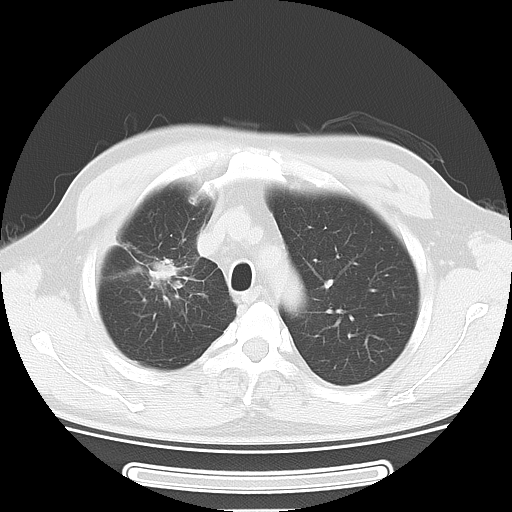
Chest CT, one axial slice; position 41 of 51 along the scan axis; lung window (W 1500 / L -600 HU); 512 × 512 image matrix, field of view 350 × 350 mm. Male patient, age 46 years. From the clinical record (not read from this slice): clinical TNM (as recorded): T3 N0 M1b.
Annotated regions visible in this slice (rectangle marked by the reading radiologist):
- lung tumour (recorded histology: adenocarcinoma): bounding box [x1, y1, x2, y2] px = [139, 248, 184, 283]